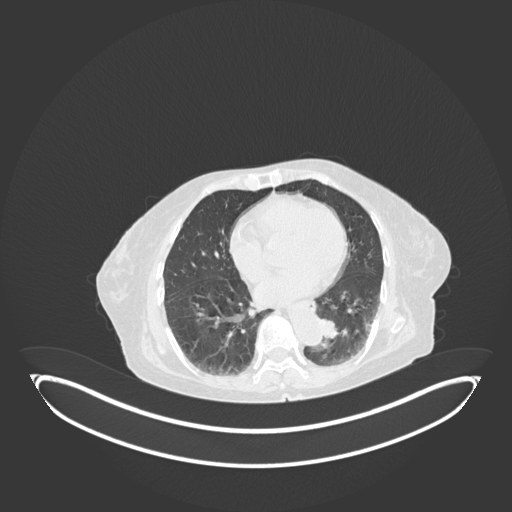
Chest CT, one axial slice. Position 35 of 189 along the scan axis. Reconstruction kernel B30f. Lung window (W 1500 / L -600 HU). 512 × 512 image matrix. Patient: female, 82 years. From the clinical record (not read from this slice): clinical TNM (as recorded): T1b N0 M1.
Structures marked on this image (rectangle marked by the reading radiologist):
- lung tumour (recorded histology: adenocarcinoma): bounding box (x1, y1, x2, y2) in pixels: (319, 311, 344, 339)